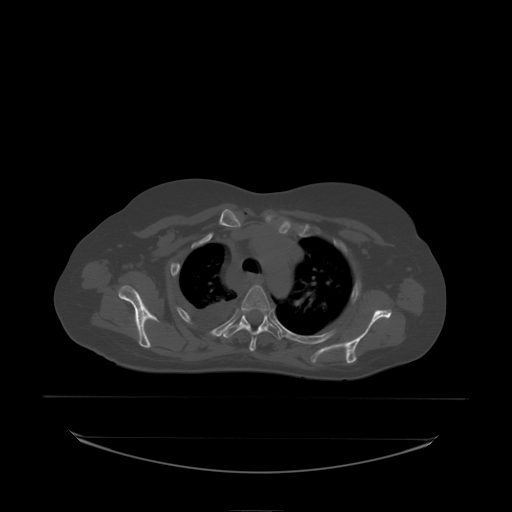
CT including the spine, one axial slice; slice 170 of 242 in the series (ordered by position); bone window (W 1800 / L 400 HU); 2.5 mm slice thickness; 512 × 512 image matrix. Patient: female, 53 years. Case-level facts recorded for this patient, not image findings: primary cancer: lung.
Structures marked on this image (semi-automatically segmented with operator editing):
- T3 vertebra: bounding box [x1, y1, x2, y2] px = [242, 285, 272, 313]
- T4 vertebra: [226, 314, 281, 338]